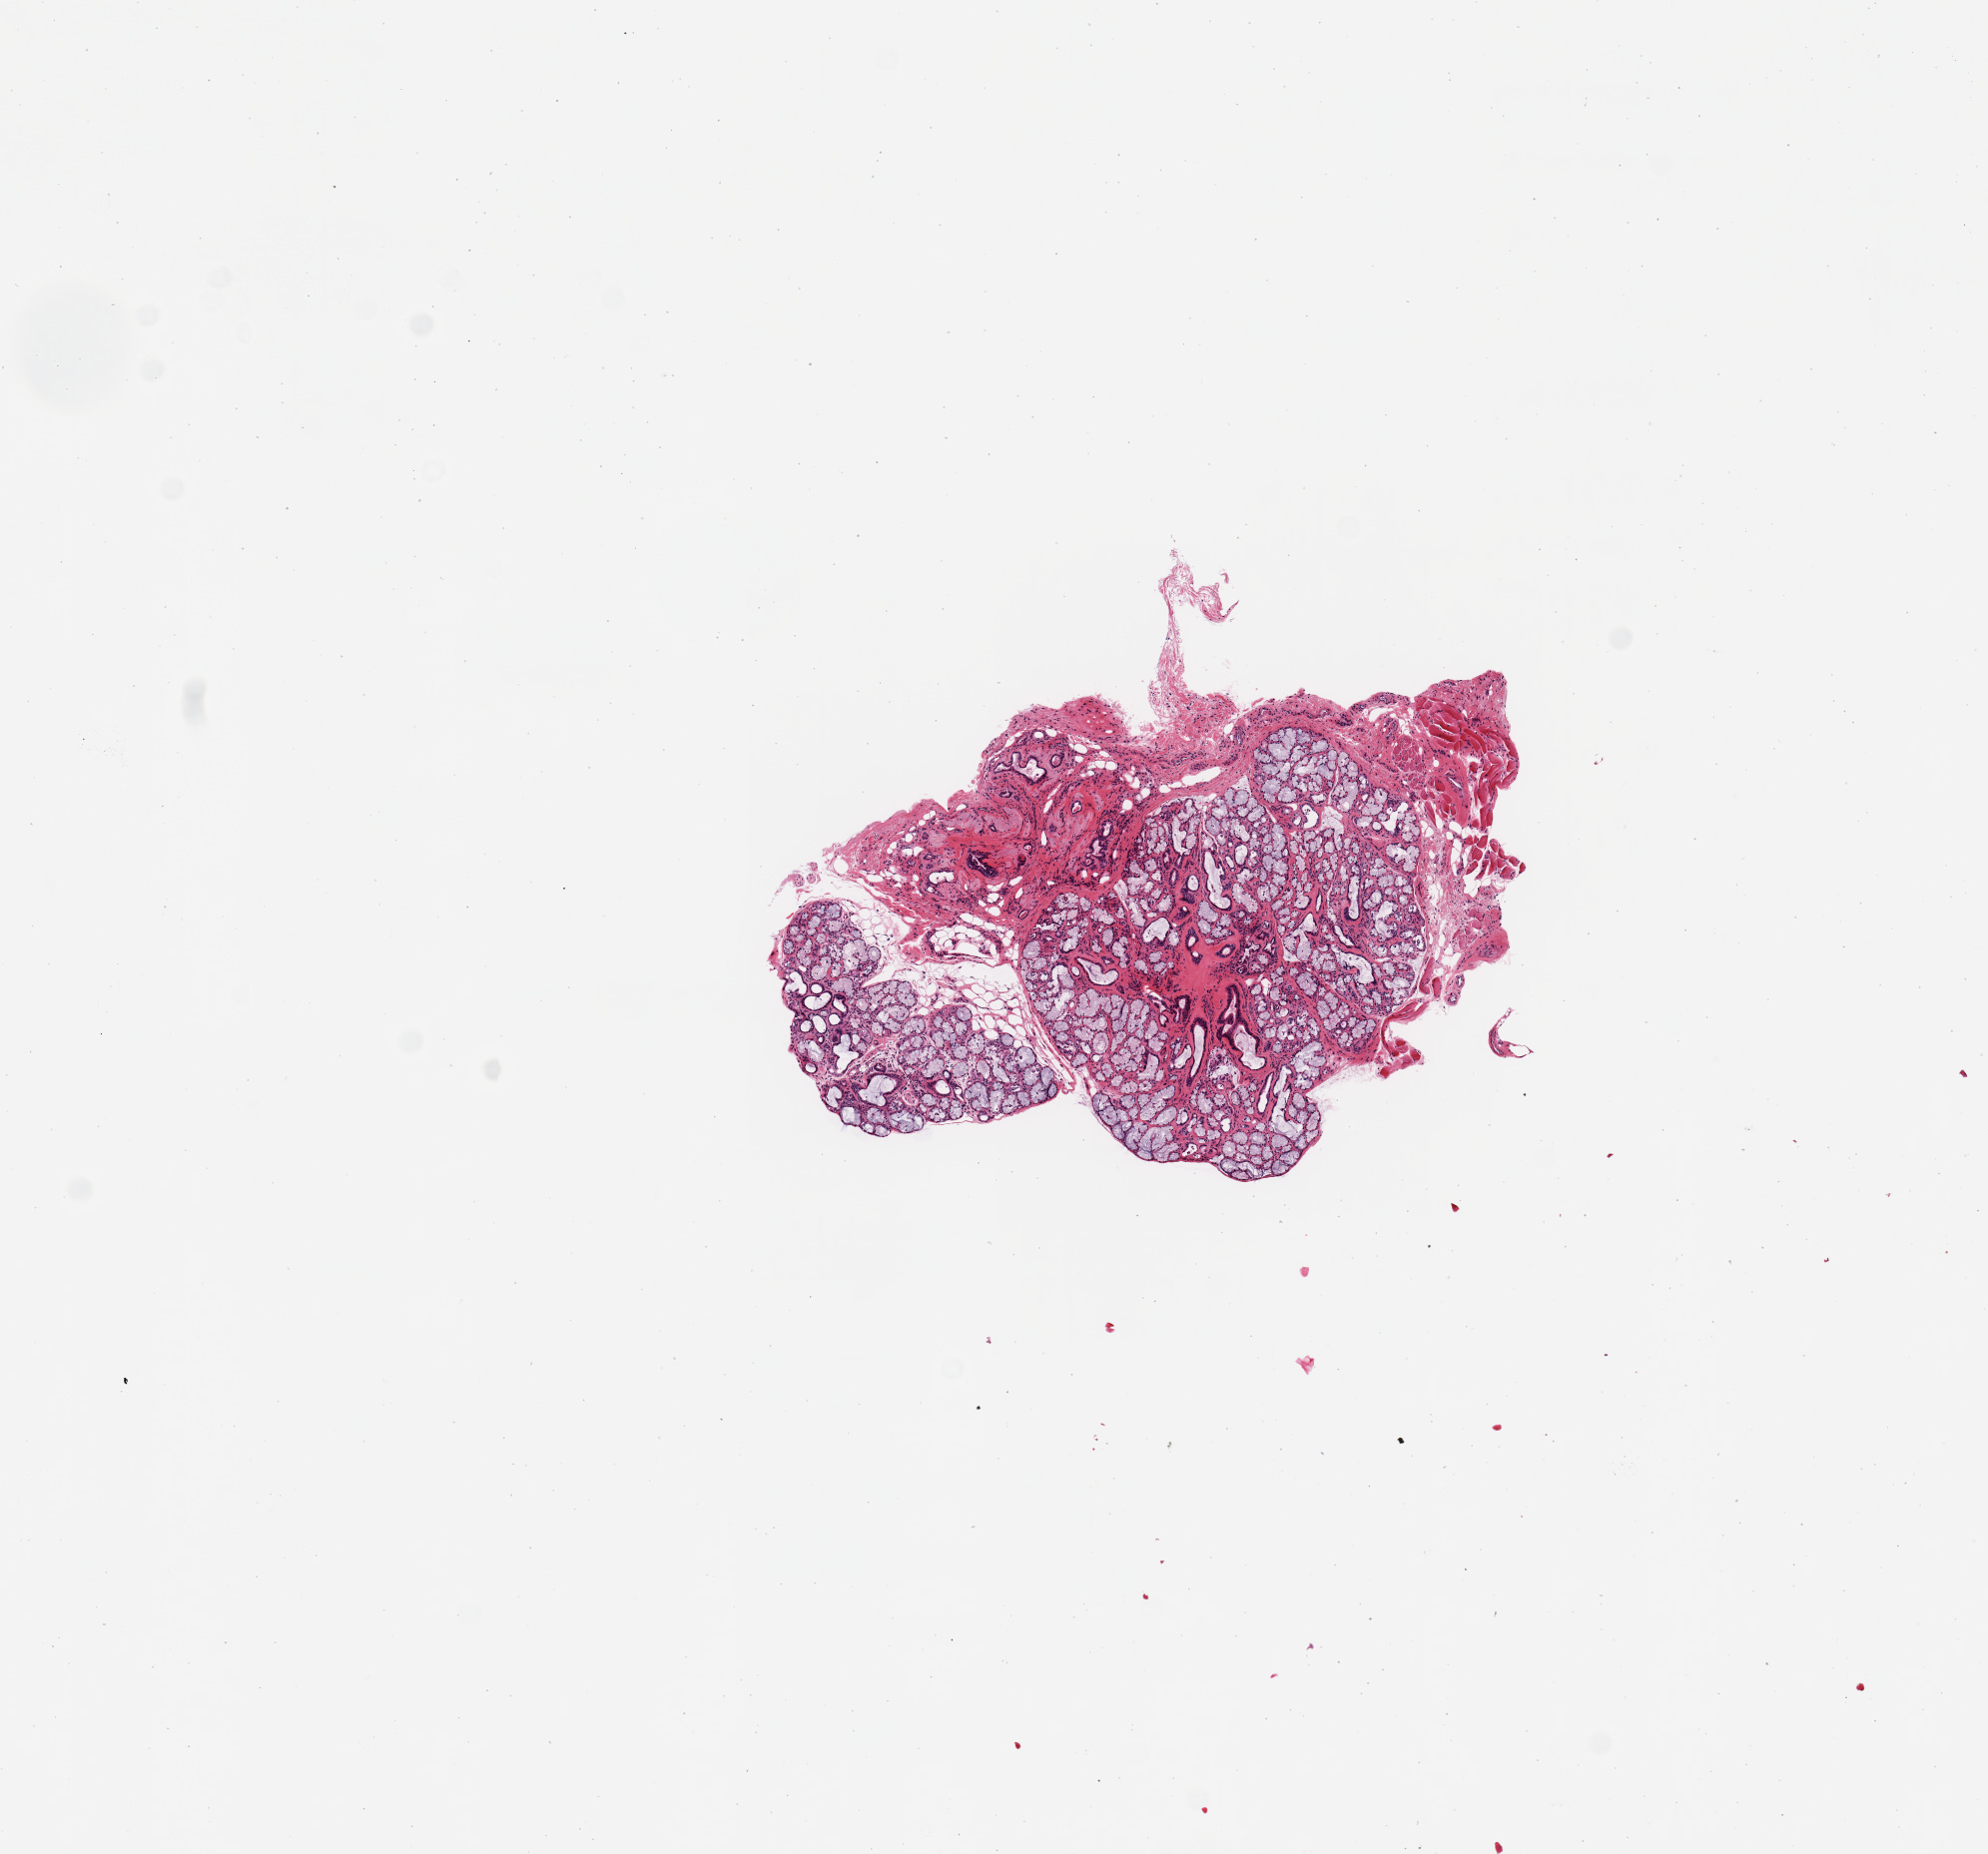
Digitized haematoxylin and eosin-stained section, brightfield — low-resolution overview of the scanned area, about 7.9 x 7.3 mm (slide scanned at 20x). PAXgene-fixed, paraffin-embedded tissue. Target tissue: minor salivary gland. Donor tissue sample. Donor sex: female.
Reviewer comment on this tissue sample: 1 piece; 80% glandular and ductal elements and attached skeletal muscle, trace of fat and fibrovascular tissue; internal fat.